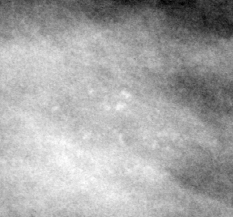
Crop from a digitized film mammogram around one marked abnormality; left breast; MLO view; BI-RADS breast density category 3 (scale 1–4).
Marked abnormality: calcifications, morphology pleomorphic, distribution clustered; BI-RADS assessment category 4; pathology (as recorded): malignant.